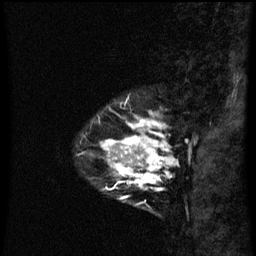
Breast MRI (dynamic contrast-enhanced), one sagittal slice; slice 12 of 60 in the series (ordered by position); dynamic contrast-enhanced series, image 2 of 3 at this slice position (ordered by acquisition); 1.5 T; TE 4.2 ms, TR 8 ms; 2.3 mm slice thickness; 256 × 256 image matrix, field of view 180 × 180 mm. Female patient, age 33 years.
Outlined on this slice (semi-automatic segmentation, software-assisted and operator-edited):
- analysis volume of interest (the breast-tissue region the enhancement analysis was run in; not a lesion): bounding box <100,120,169,199> (left, top, right, bottom; pixels)
- tumour enhancement mask (voxels above the 70 % enhancement threshold inside the analysis volume of interest): <103,120,169,187>